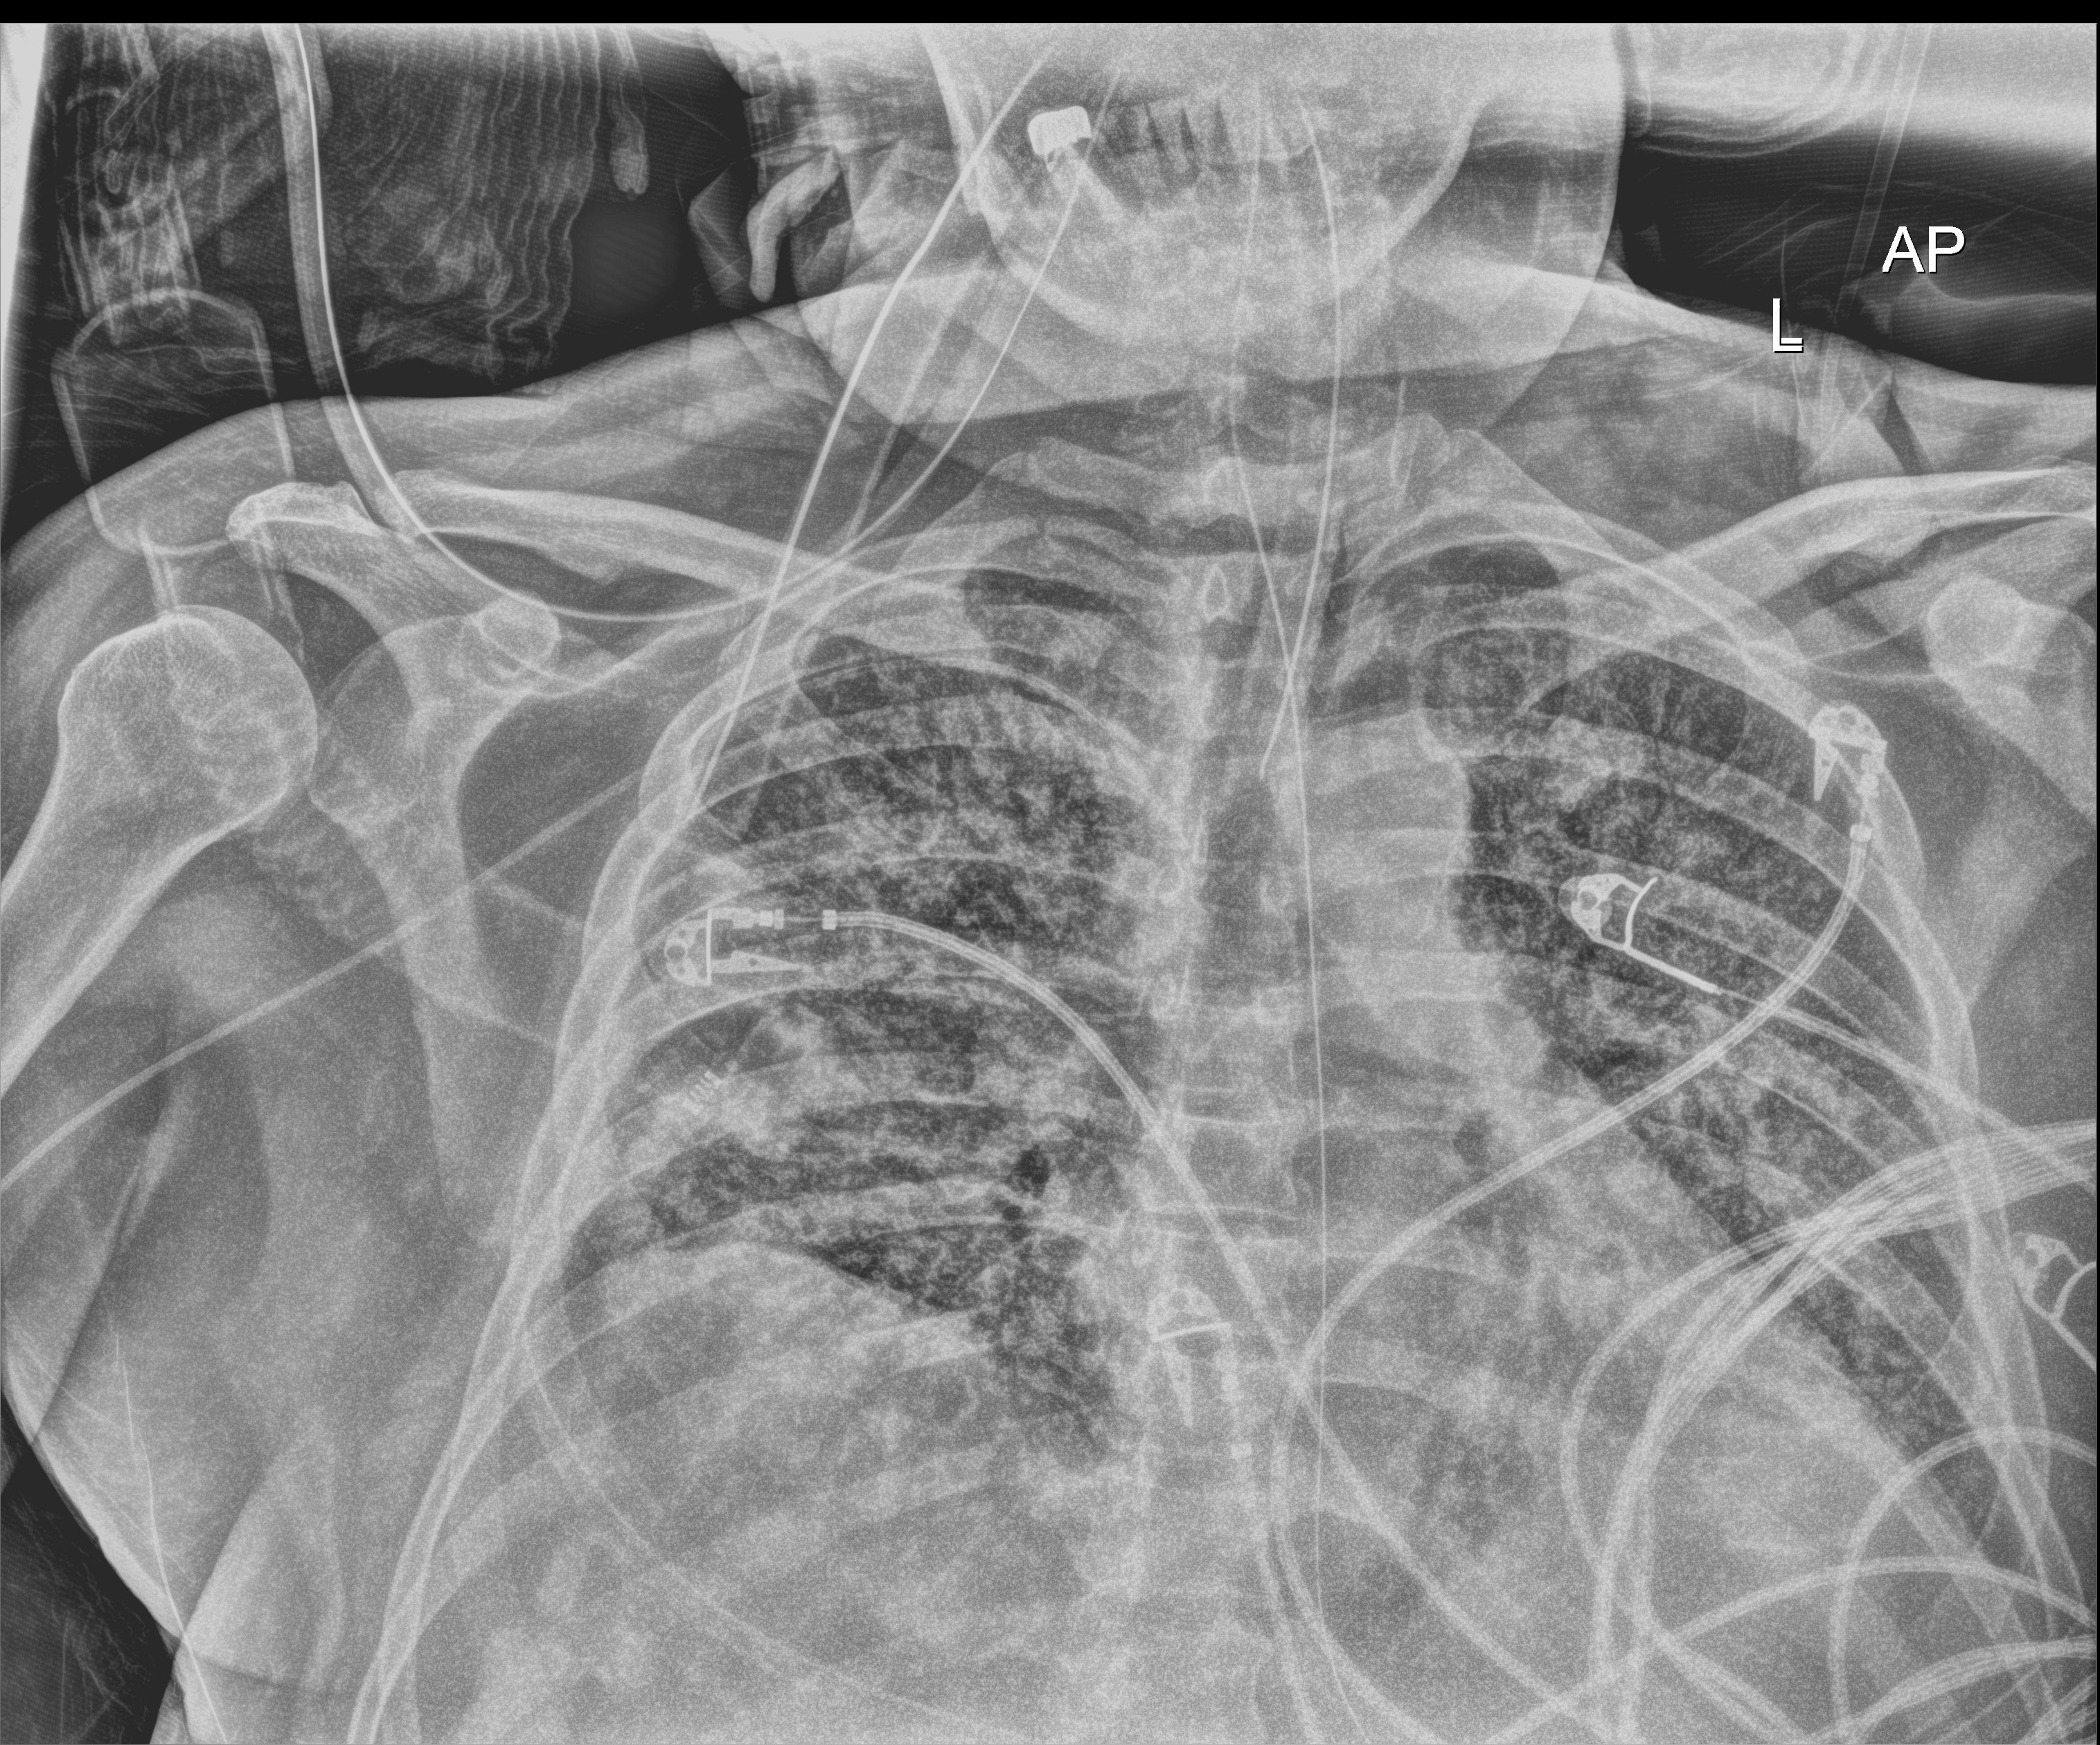
Chest X-ray (portable); anteroposterior (AP) projection. Patient hospitalised with COVID-19; male, aged 18–59 years.
From the hospital-stay record, not from the radiograph (when in the stay this image was taken is not recorded): chronic kidney disease (admission record): no; COPD (admission record): no.